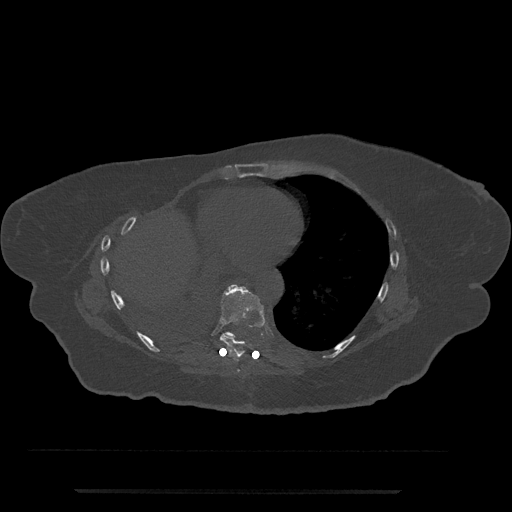
CT including the spine, one axial slice; position 380 of 797 along the scan axis; bone window (W 1800 / L 400 HU); 0.5 mm slice thickness; 512 × 512 image matrix, field of view 440 × 440 mm. Female patient, age 51 years. Case-level facts recorded for this patient, not image findings: primary cancer: neuro; vertebrae with lytic lesions (as recorded): T8.
Outlined on this slice (semi-automatically segmented with operator editing):
- T7 vertebra: bounding box (x1, y1, x2, y2) in pixels: (237, 369, 240, 373)
- T8 vertebra: (220, 284, 265, 359)
- T9 vertebra: (224, 286, 264, 340)